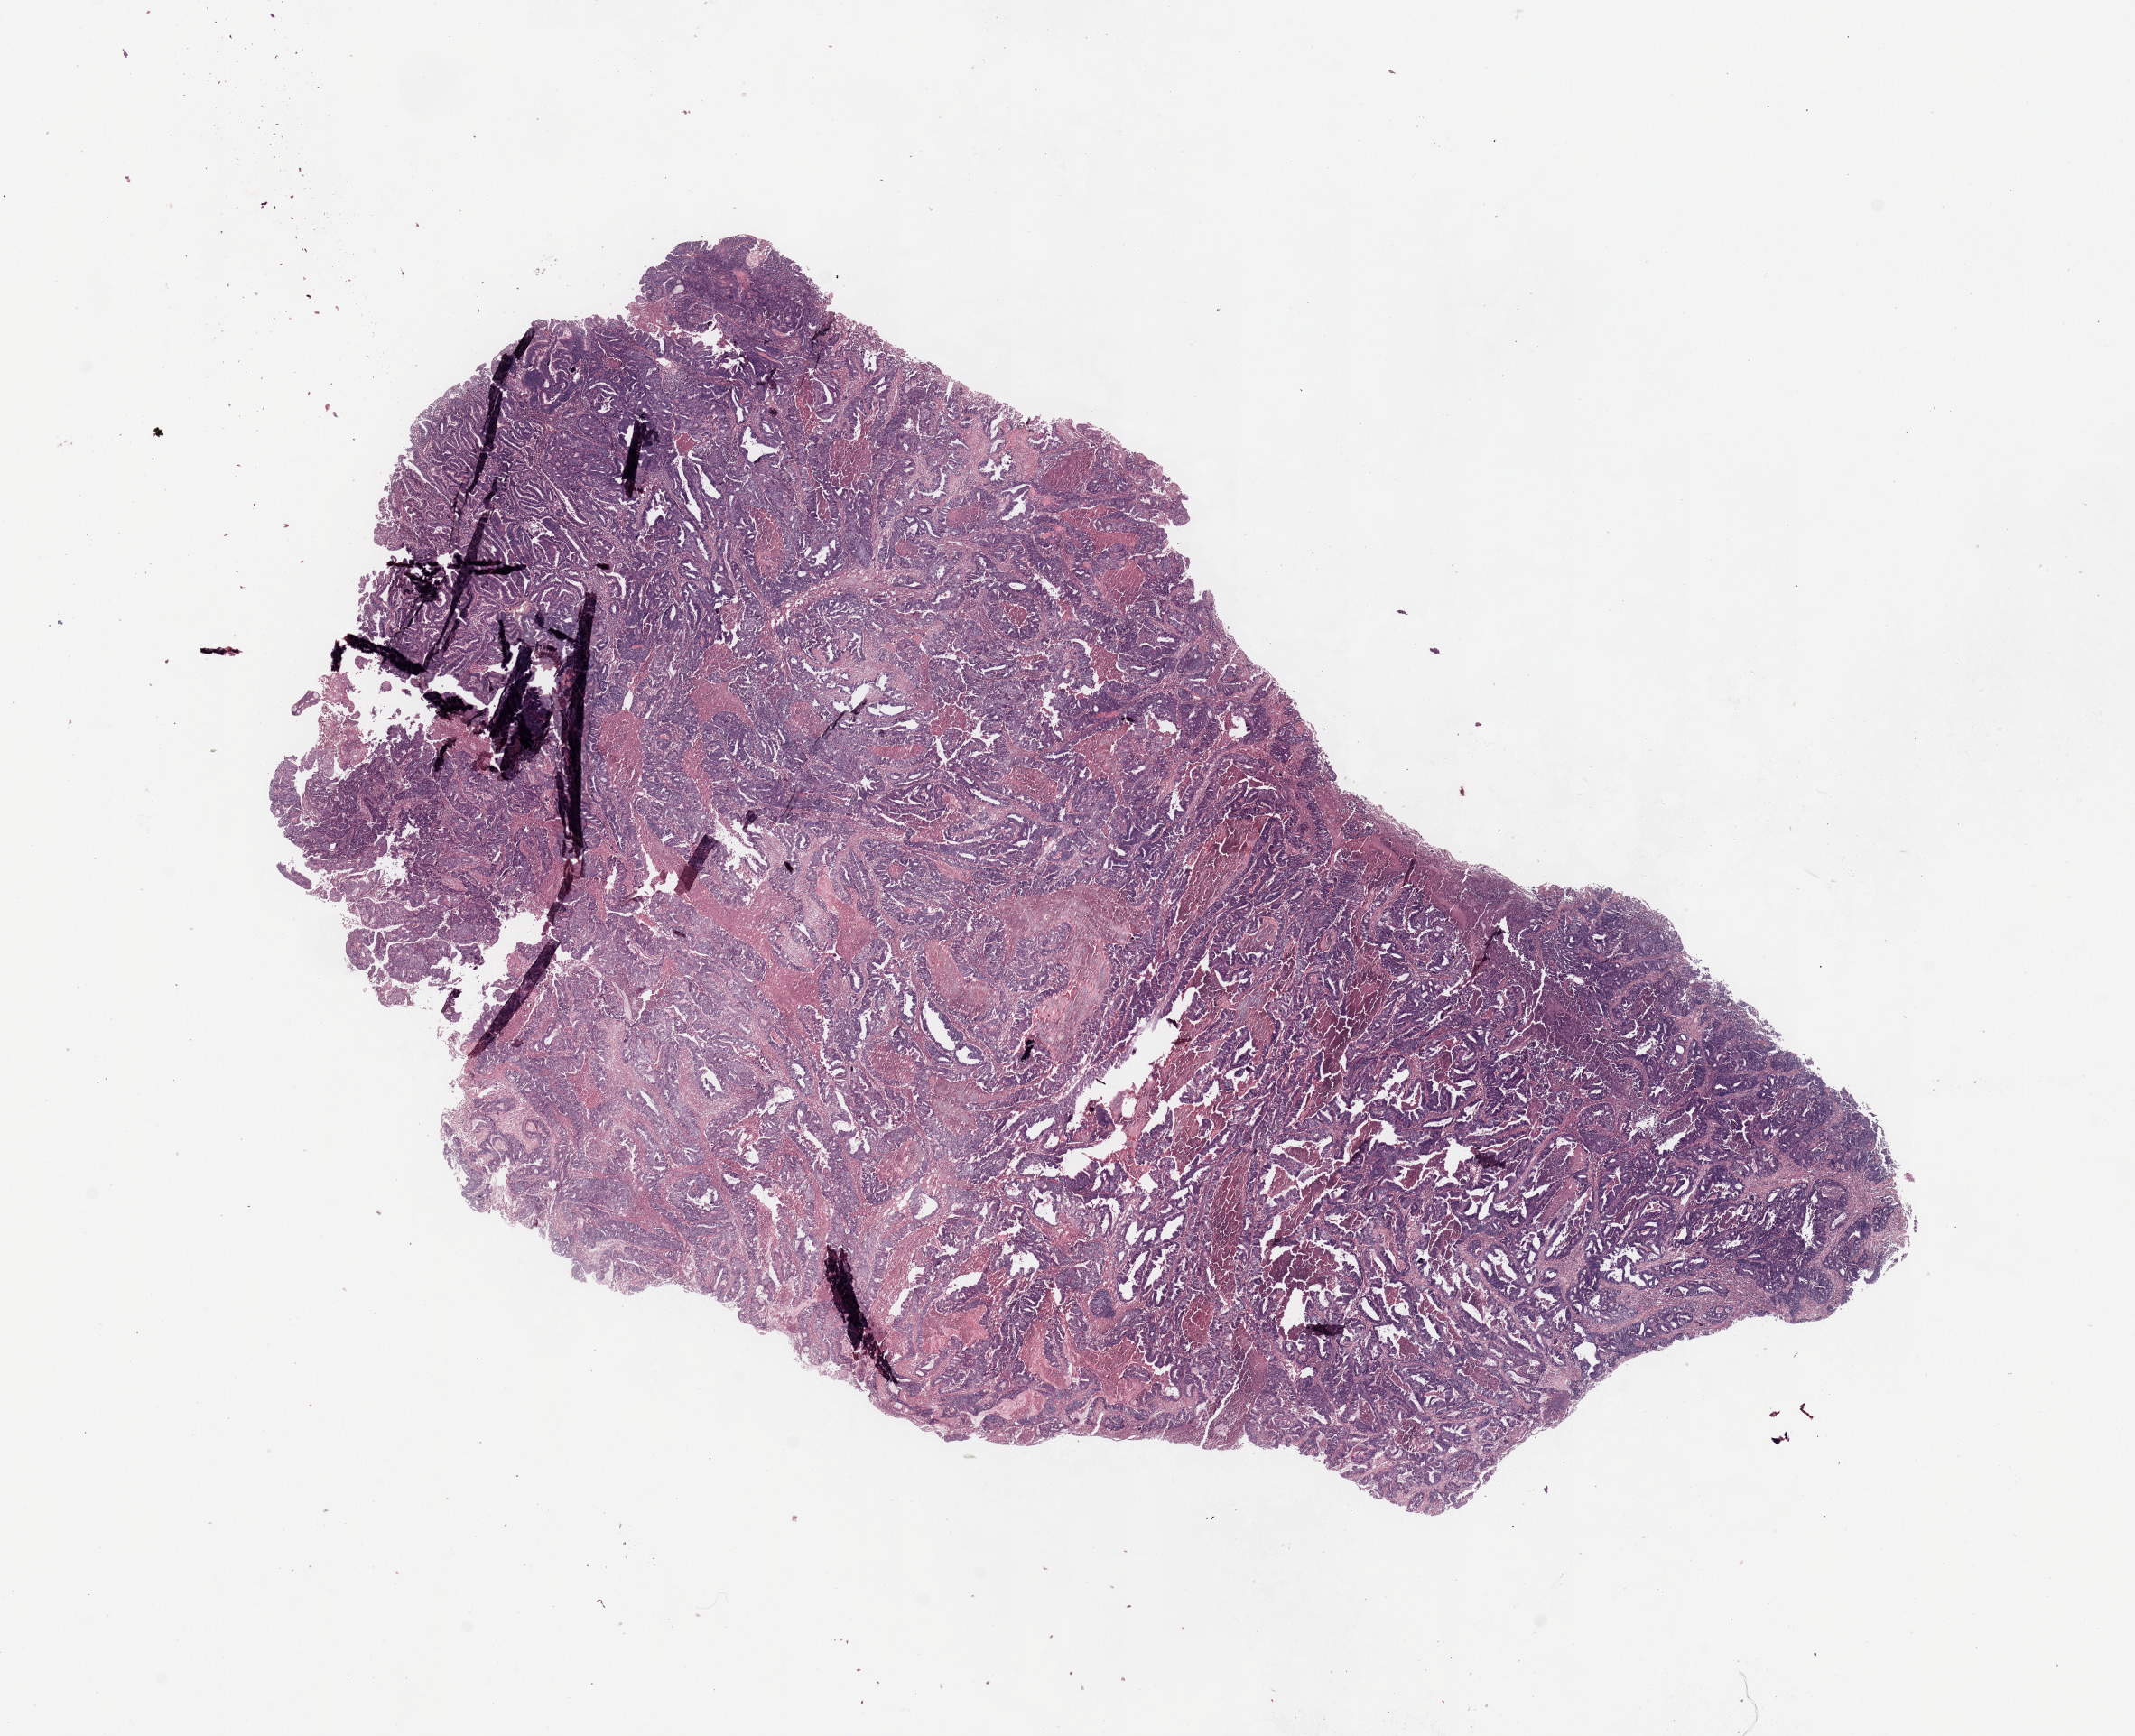
Digitized H&E tissue section (whole slide), shown as a low-resolution overview of the whole scanned area (about 18.7 x 15.2 mm). Uterus, tumour tissue. 62-year-old female patient. Histologic grade: G2 (moderately differentiated).
• diagnosis: Endometrioid adenocarcinoma, NOS
• AJCC pathologic stage: I